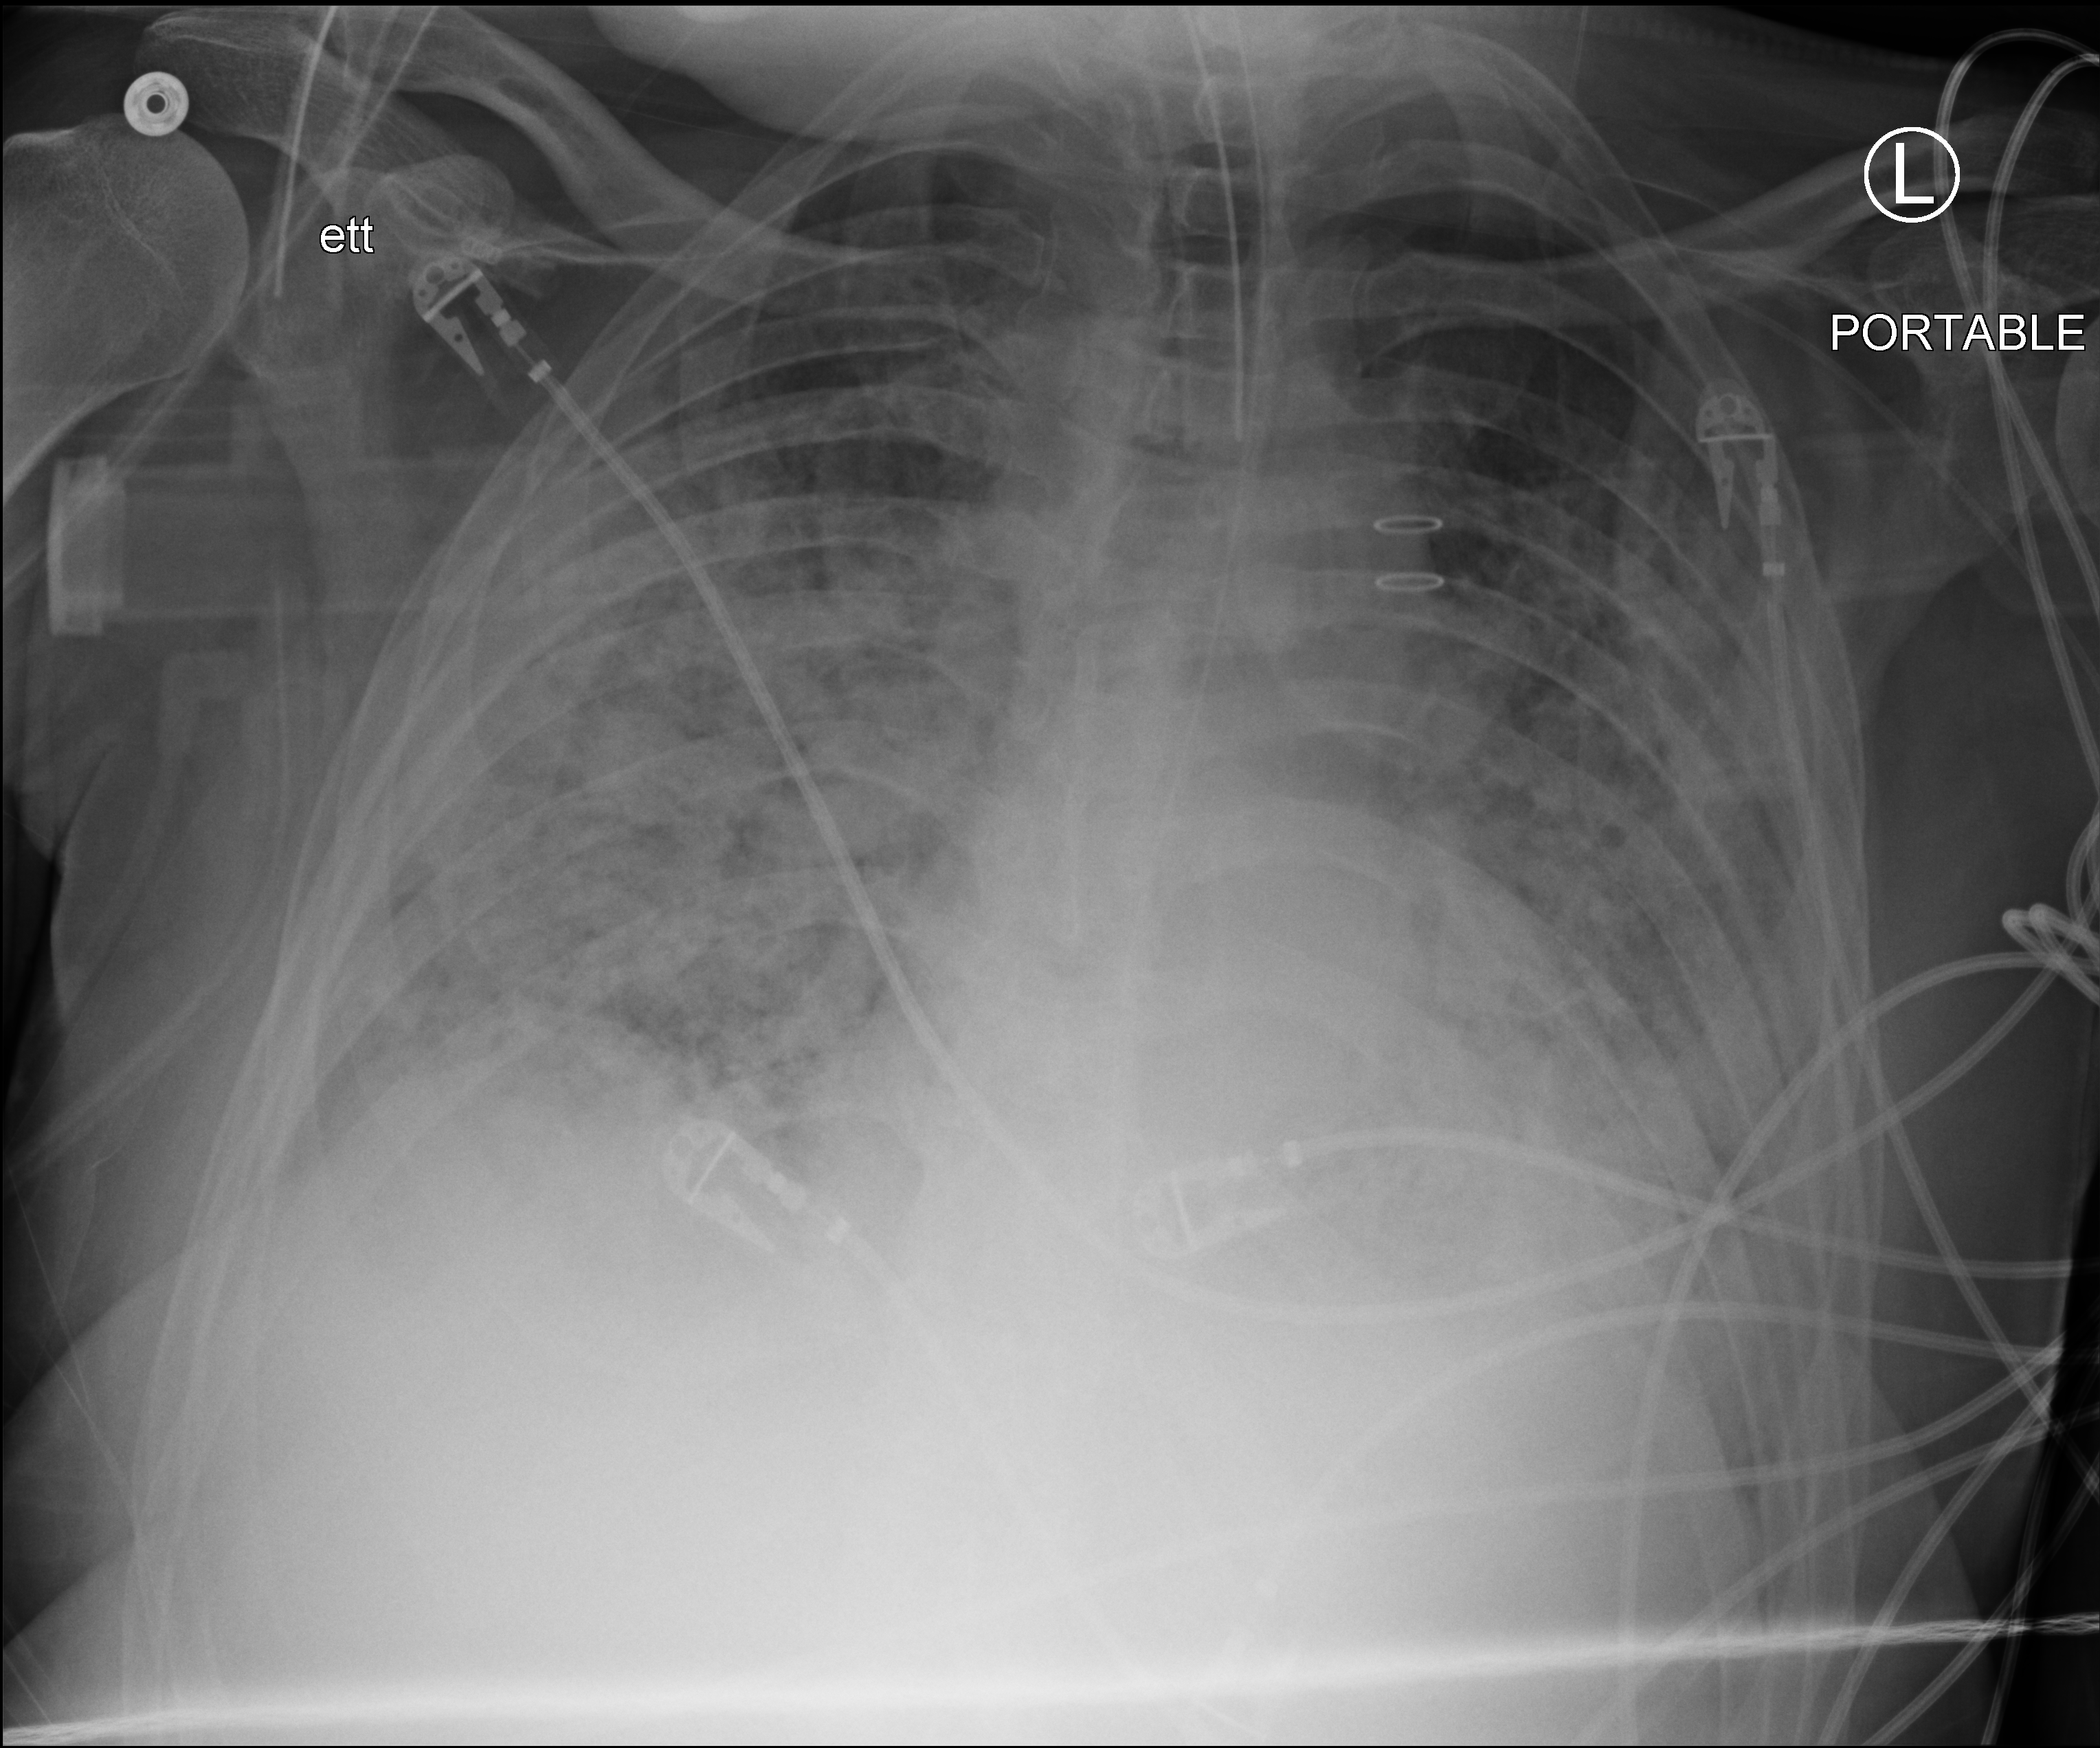
Bedside chest radiograph (computed radiography); anteroposterior (AP) projection. Male patient hospitalised with COVID-19, age 18–59 years.
Admission-level facts for this patient (not findings on this image; timing relative to this image not recorded): hypertension (admission record): no.